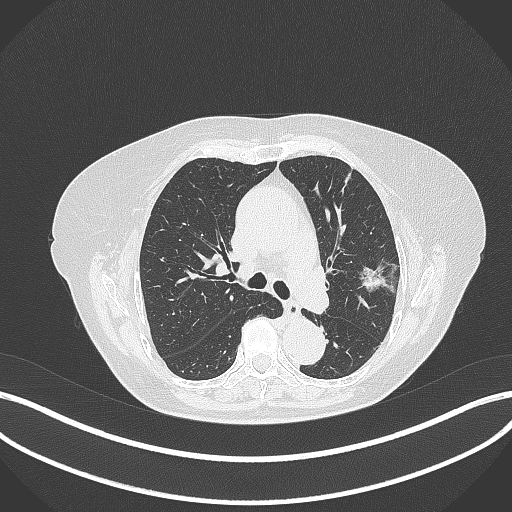
Chest CT, one axial slice; slice 209 of 316 in the series (ordered by position); 120 kVp; lung window (W 1500 / L -600 HU); 1 mm slice thickness; 512 × 512 image matrix, field of view 400 × 400 mm. Patient: female, 75 years. Case-level facts recorded for this patient, not image findings: clinical TNM (as recorded): T1c N0 M0.
Annotated regions visible in this slice (rectangle marked by the reading radiologist):
- lung tumour (recorded histology: adenocarcinoma): box from (x=357, y=261) to (x=386, y=300) px